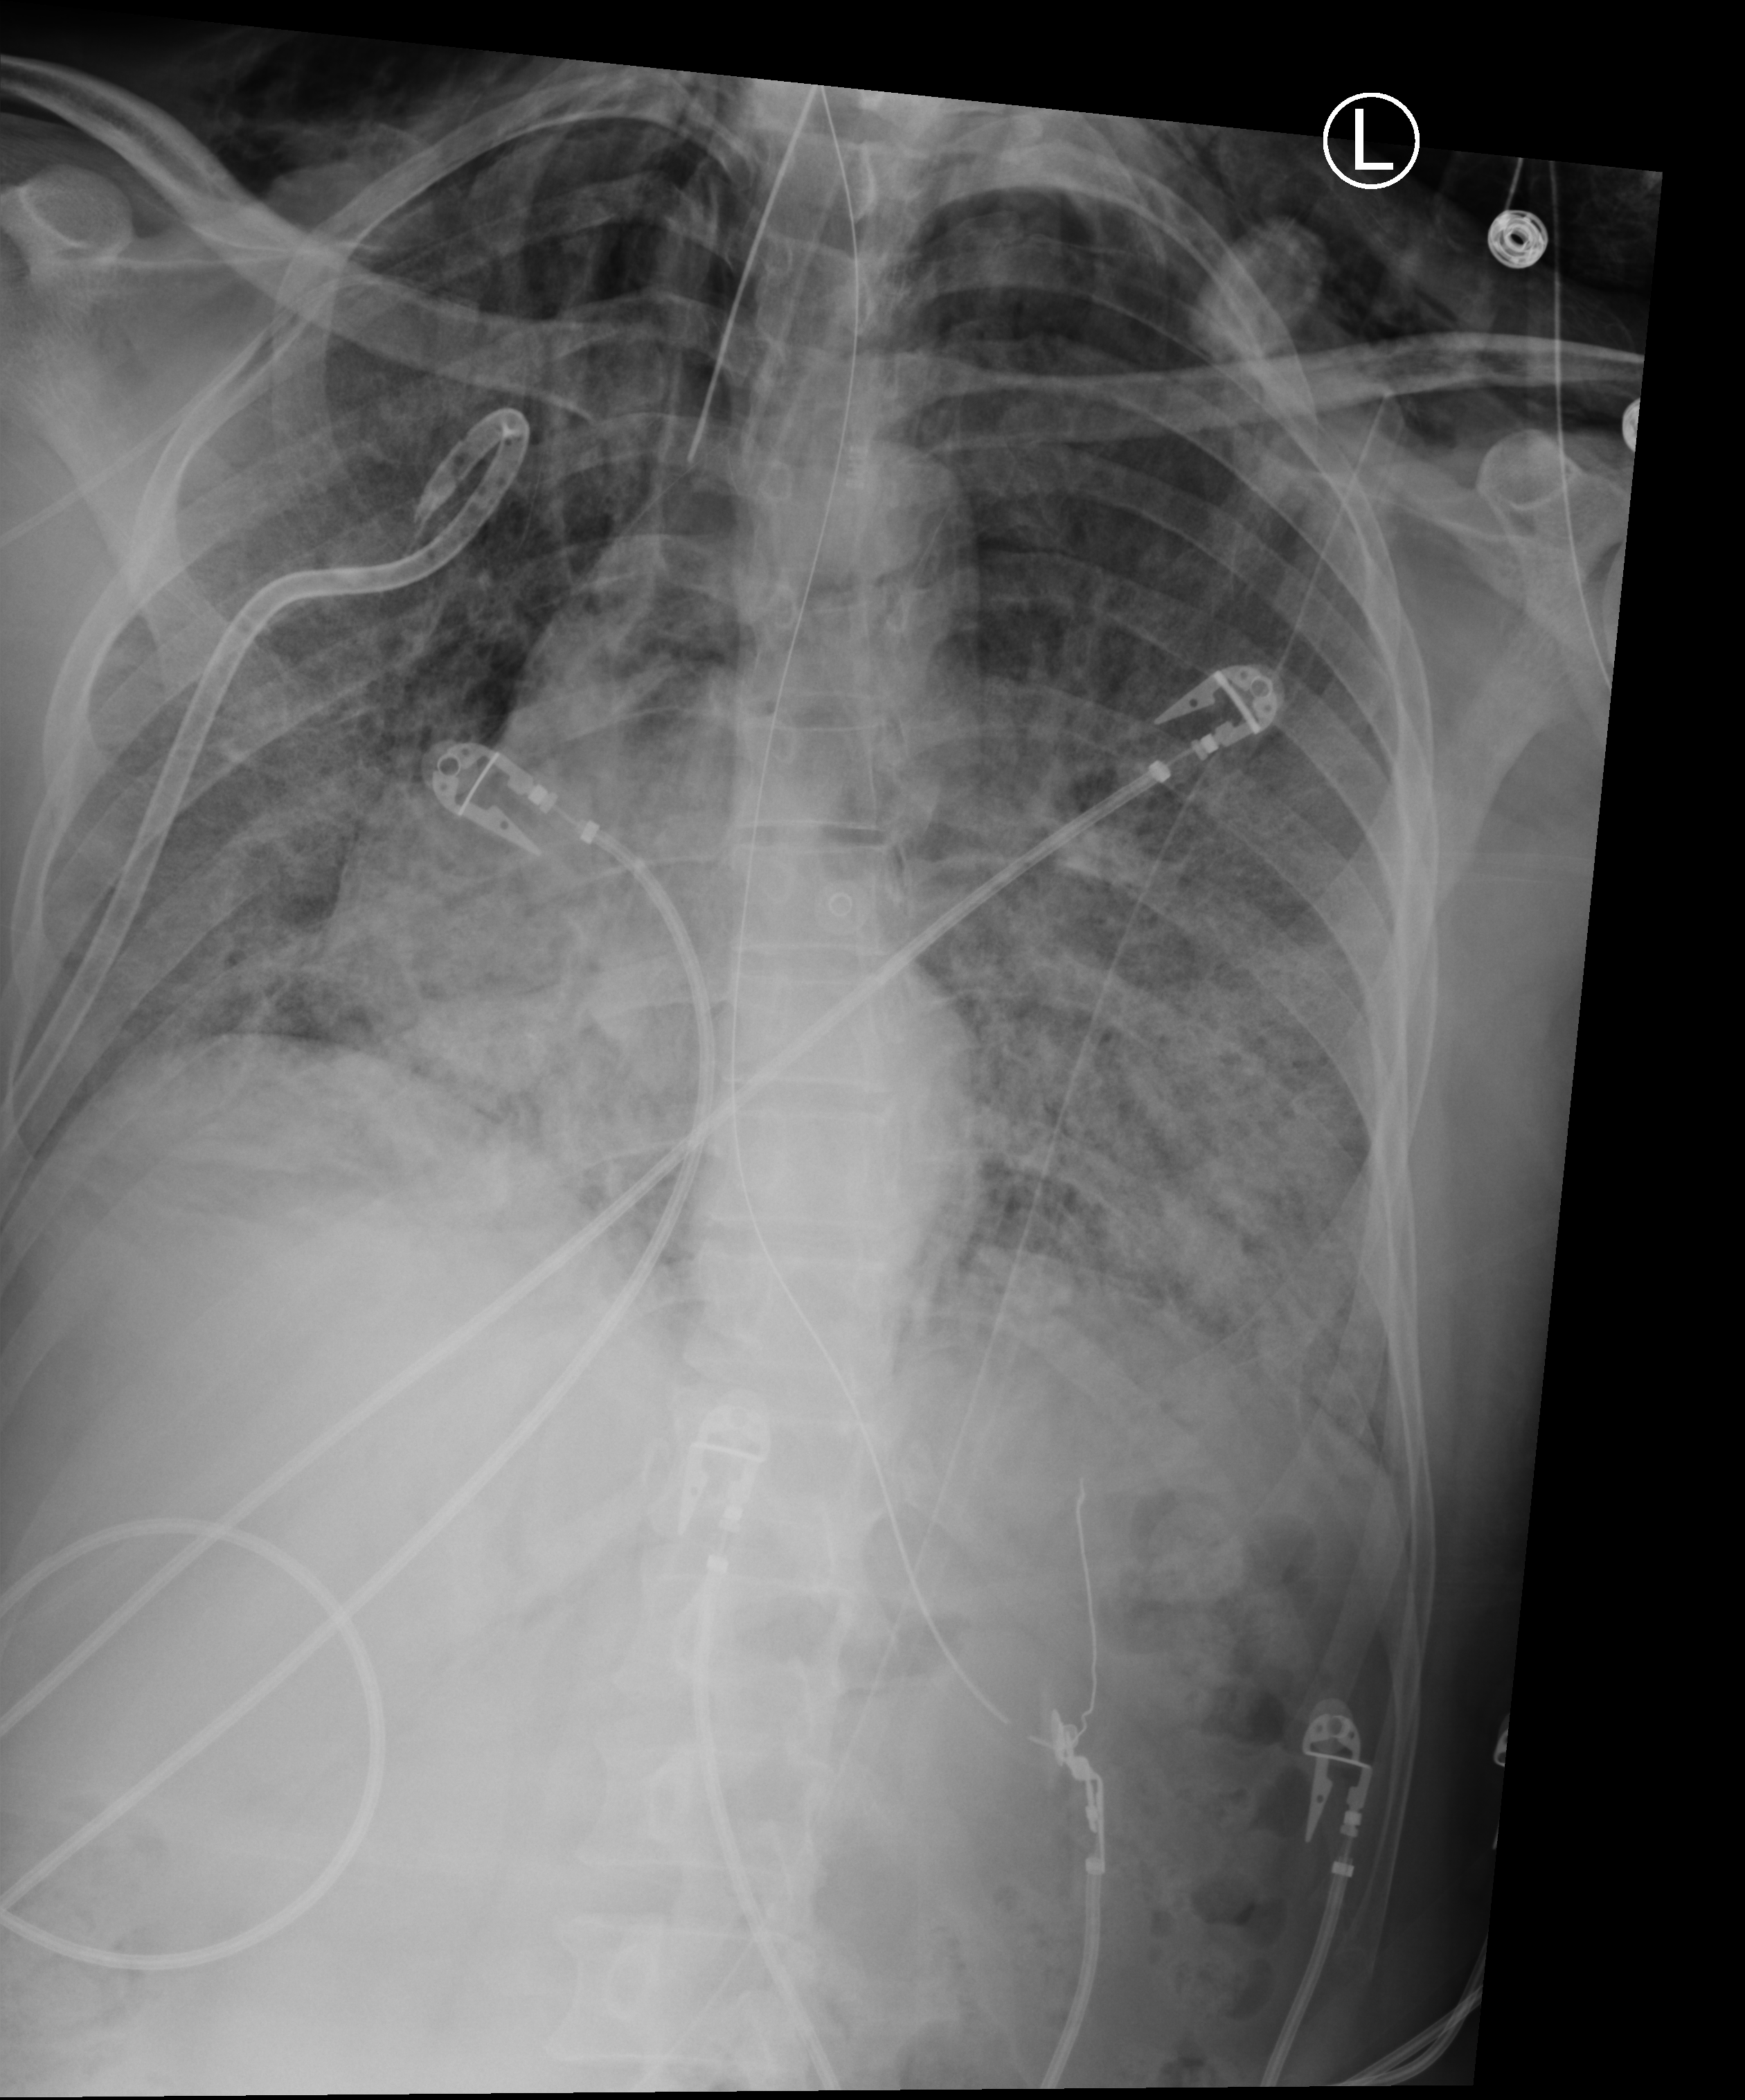
Portable chest radiograph; anteroposterior (AP) projection. Patient hospitalised with COVID-19, aged 18–59 years.
Admission-level facts for this patient (not findings on this image; timing relative to this image not recorded): mechanically ventilated during this hospital stay: yes; other chronic lung disease (admission record): no; admitted to intensive care during this hospital stay: yes.